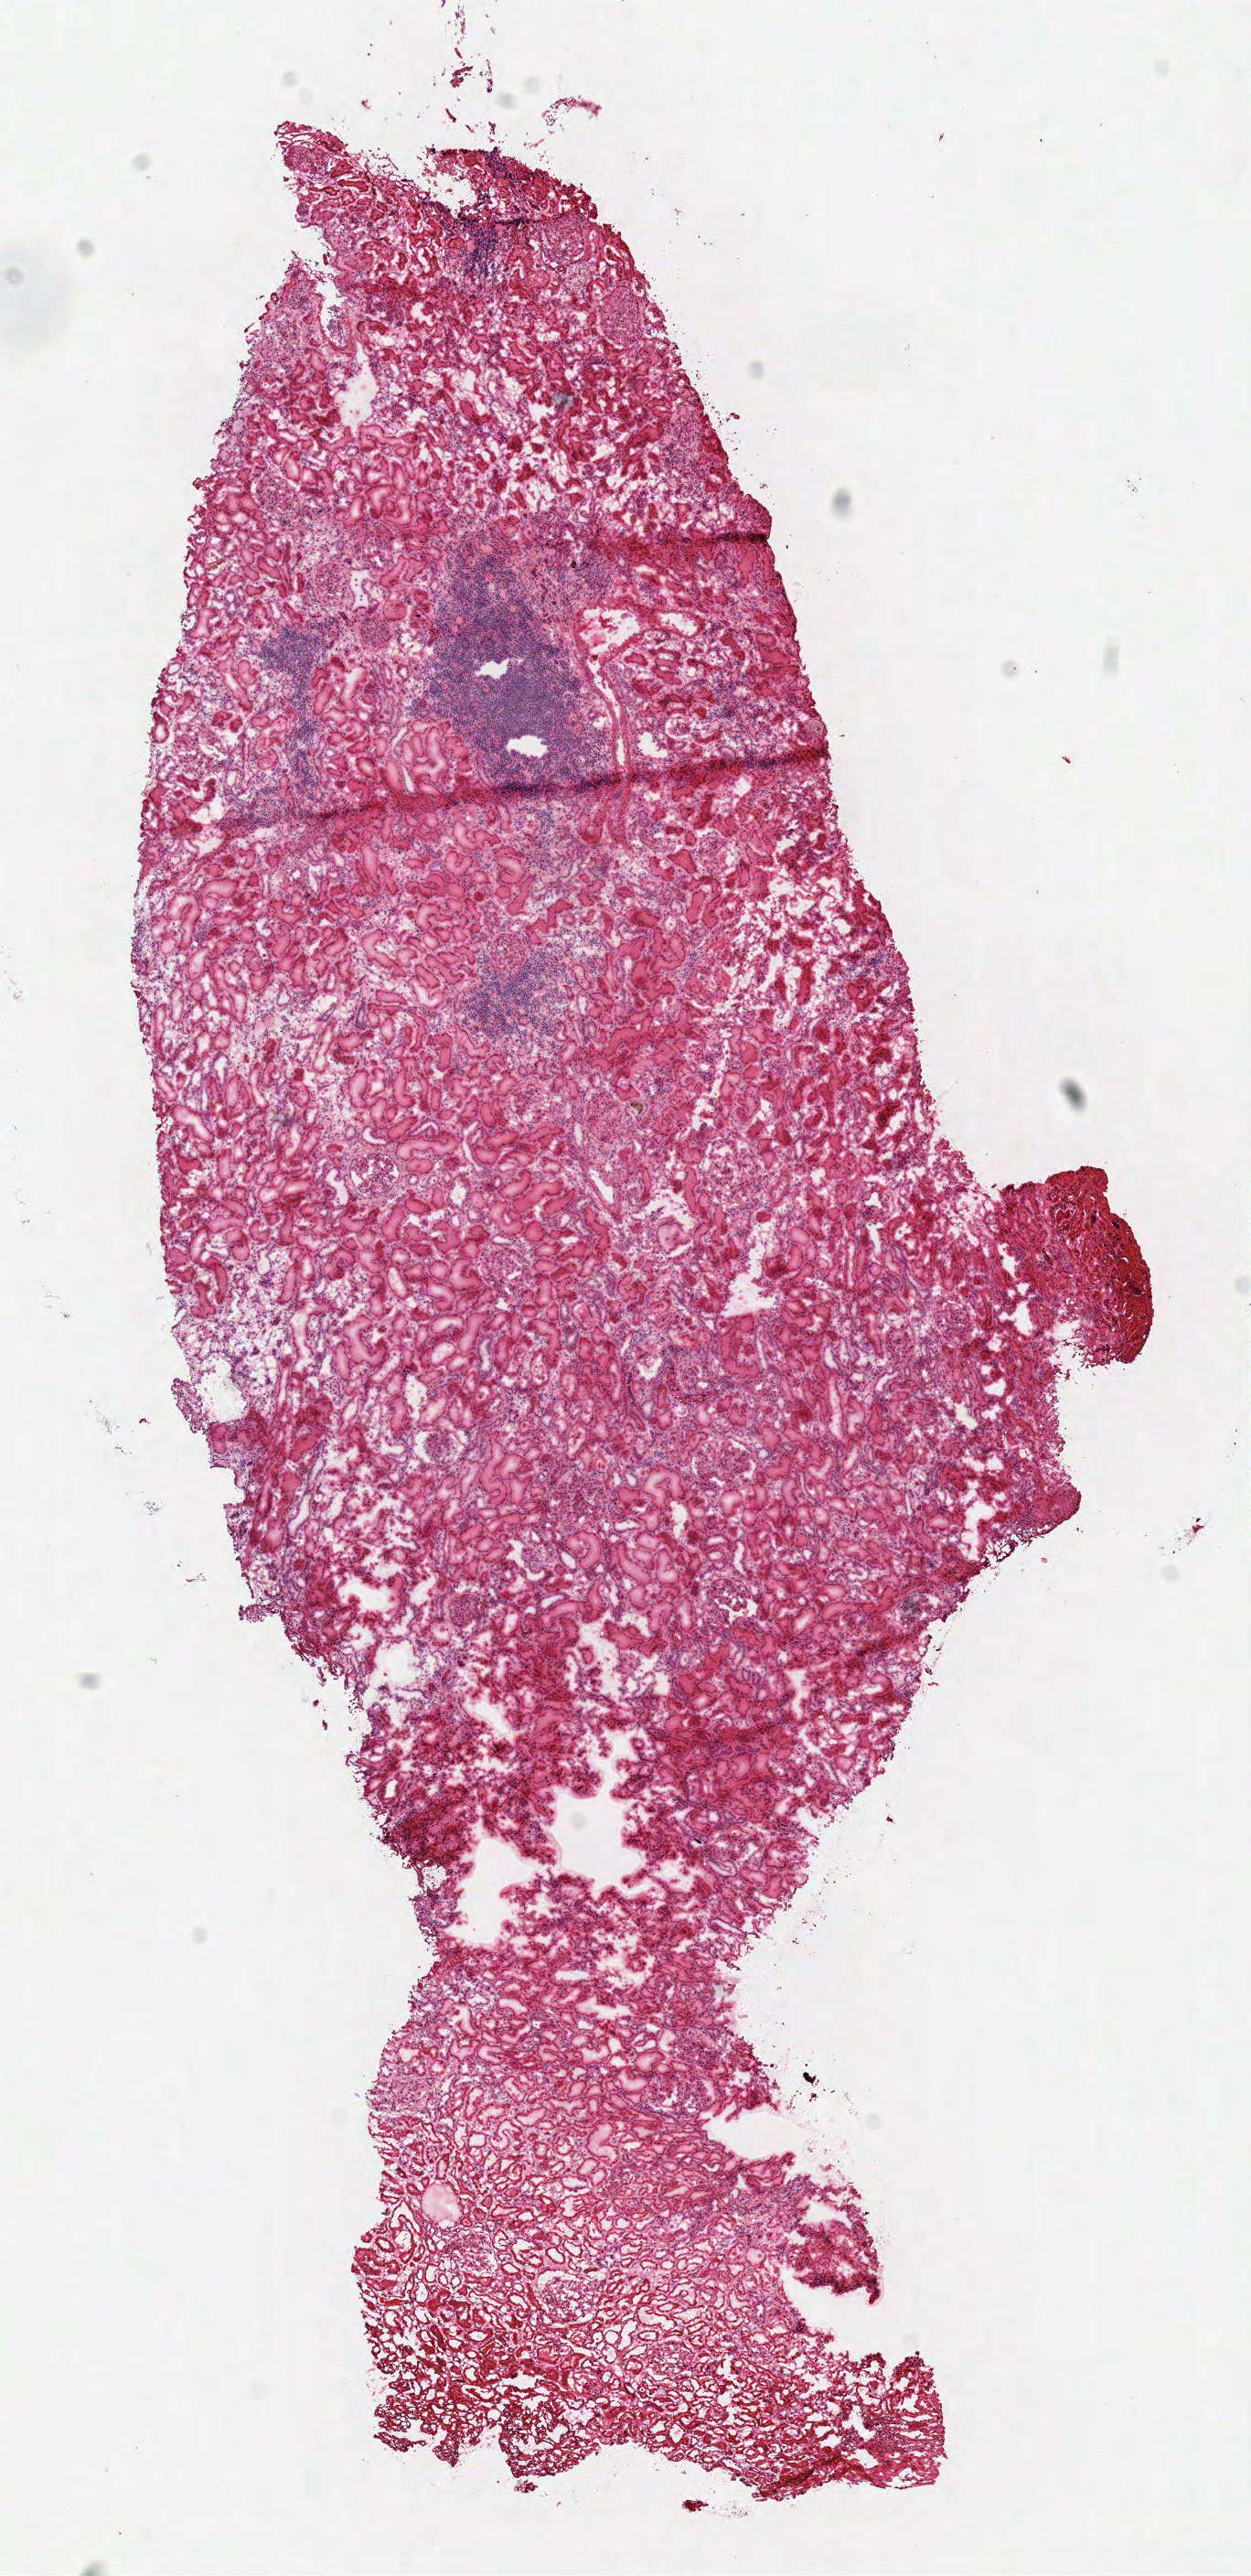
Whole-slide histology image, Hematoxylin and eosin (H&E) stained — low-resolution overview of the scanned area, about 5.4 x 11.1 mm (from a 40x scan); frozen section from the top of the tissue portion; solid tissue normal (non-tumour tissue) sample from the kidney. Patient: male, age at initial diagnosis 45 years.
This section: solid tissue normal (non-tumour) sample from the same patient. Patient diagnosis: Papillary adenocarcinoma, NOS.